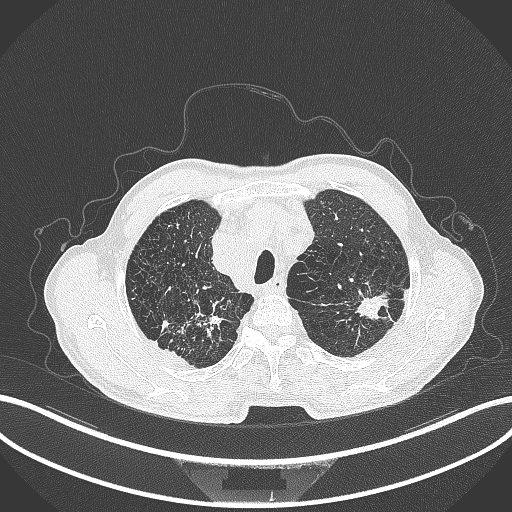
Chest CT, one axial slice; position 370 of 463 along the scan axis; 120 kVp; lung window (W 1500 / L -600 HU); 512 × 512 image matrix, field of view 400 × 400 mm. Male patient, age 74 years. From the clinical record (not read from this slice): clinical TNM (as recorded): T2a N1 M0.
Structures marked on this image (bounding box drawn by a radiologist):
- lung tumour (recorded histology: adenocarcinoma): box from (x=351, y=288) to (x=390, y=326) px